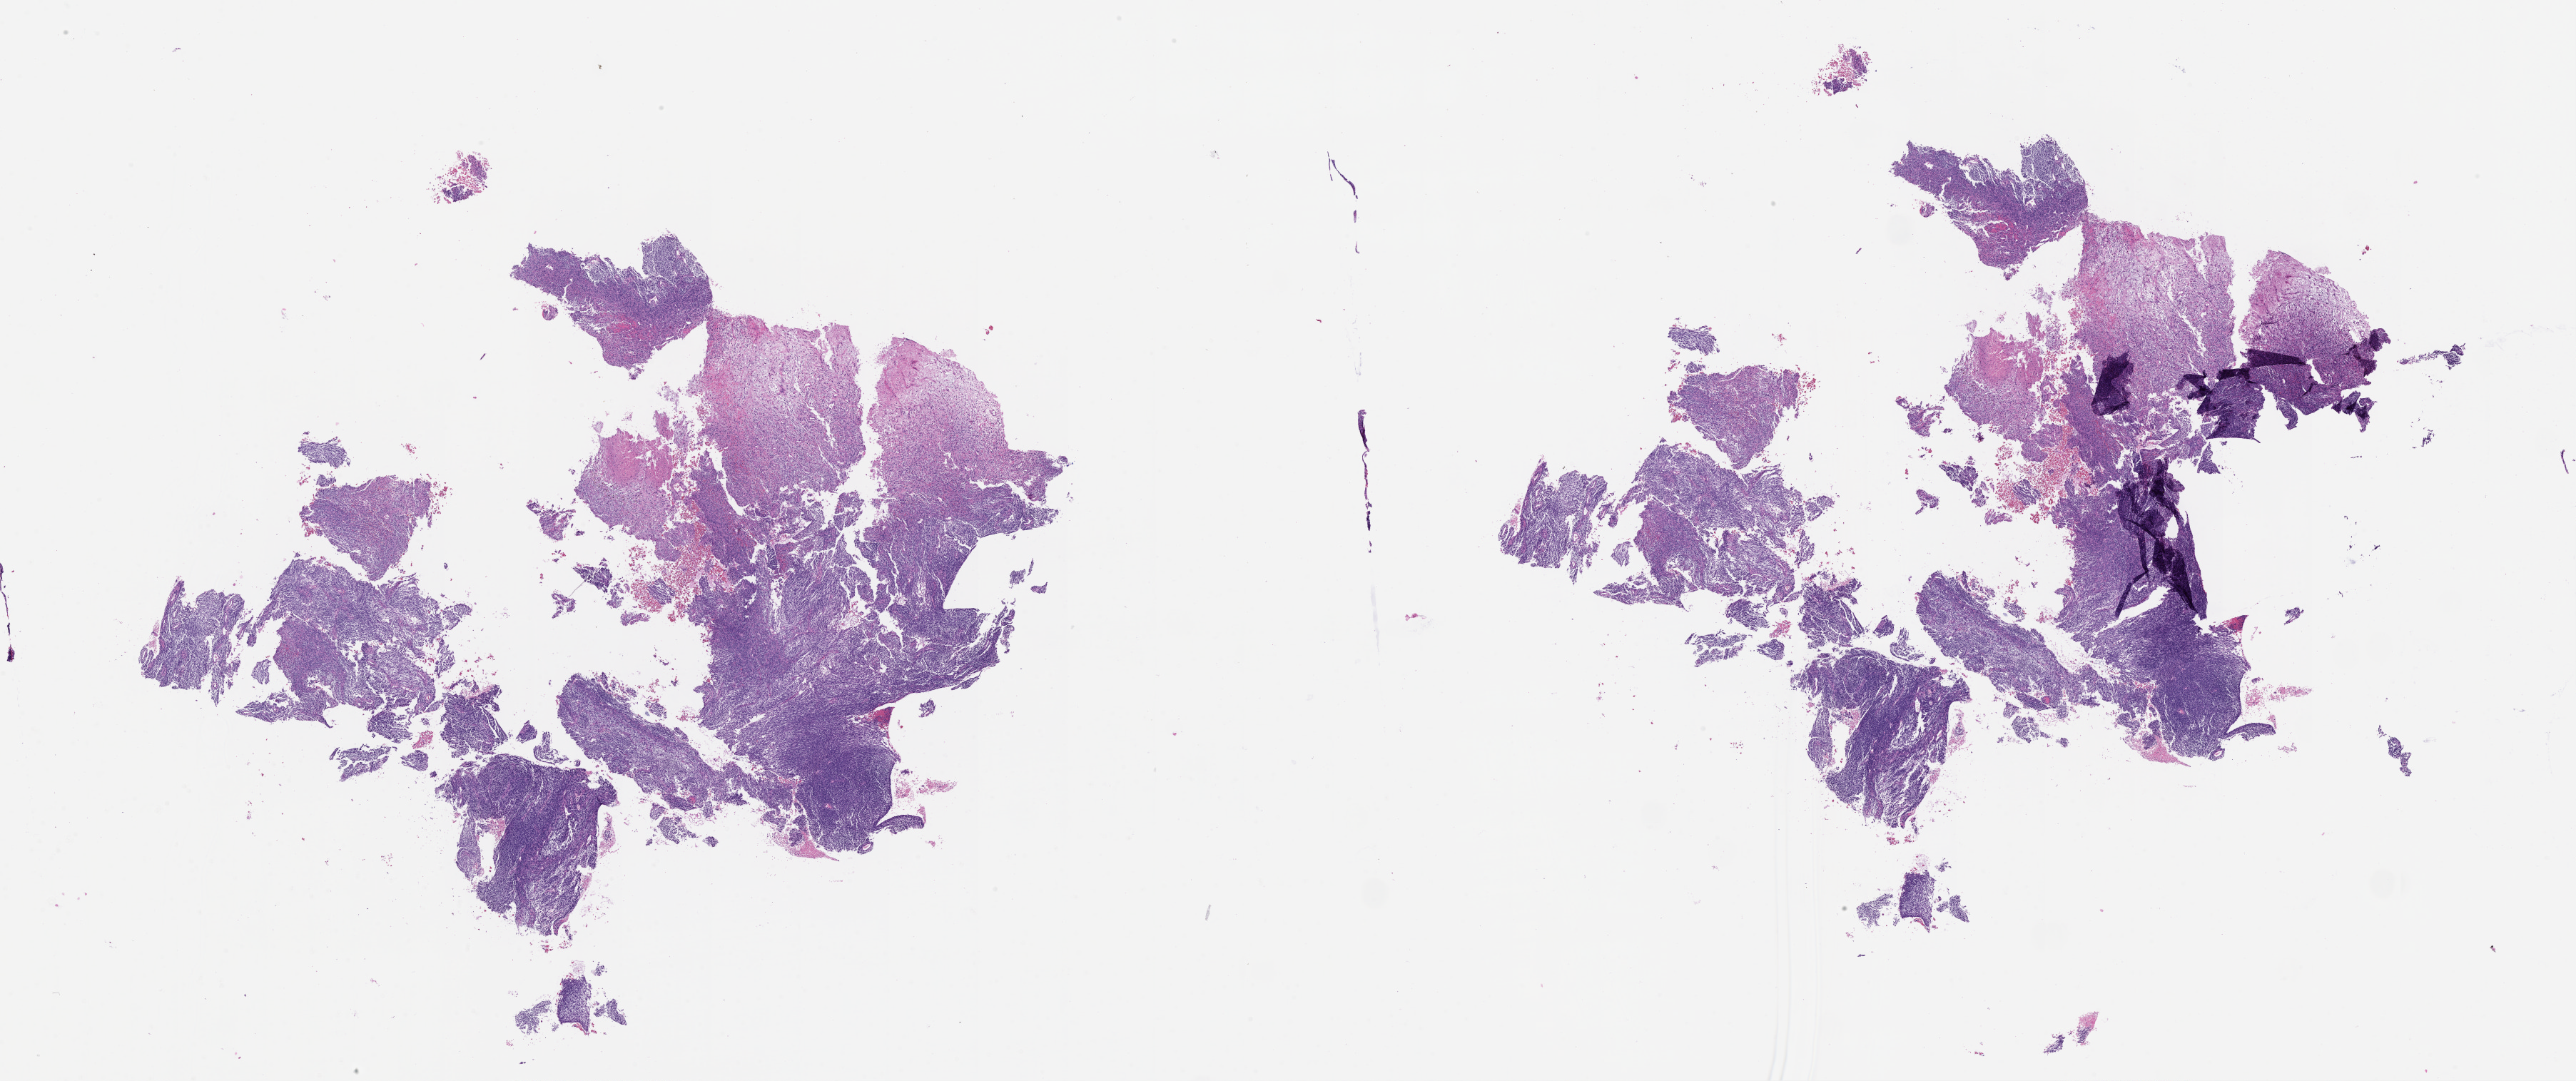
Digitized H&E-stained tissue section (whole slide), shown as a low-resolution overview of the whole scanned area (about 29.1 x 12.2 mm, slide scanned at 20x).
Patient diagnosis (cohort enrolment): sarcoma (site not recorded at cohort level).